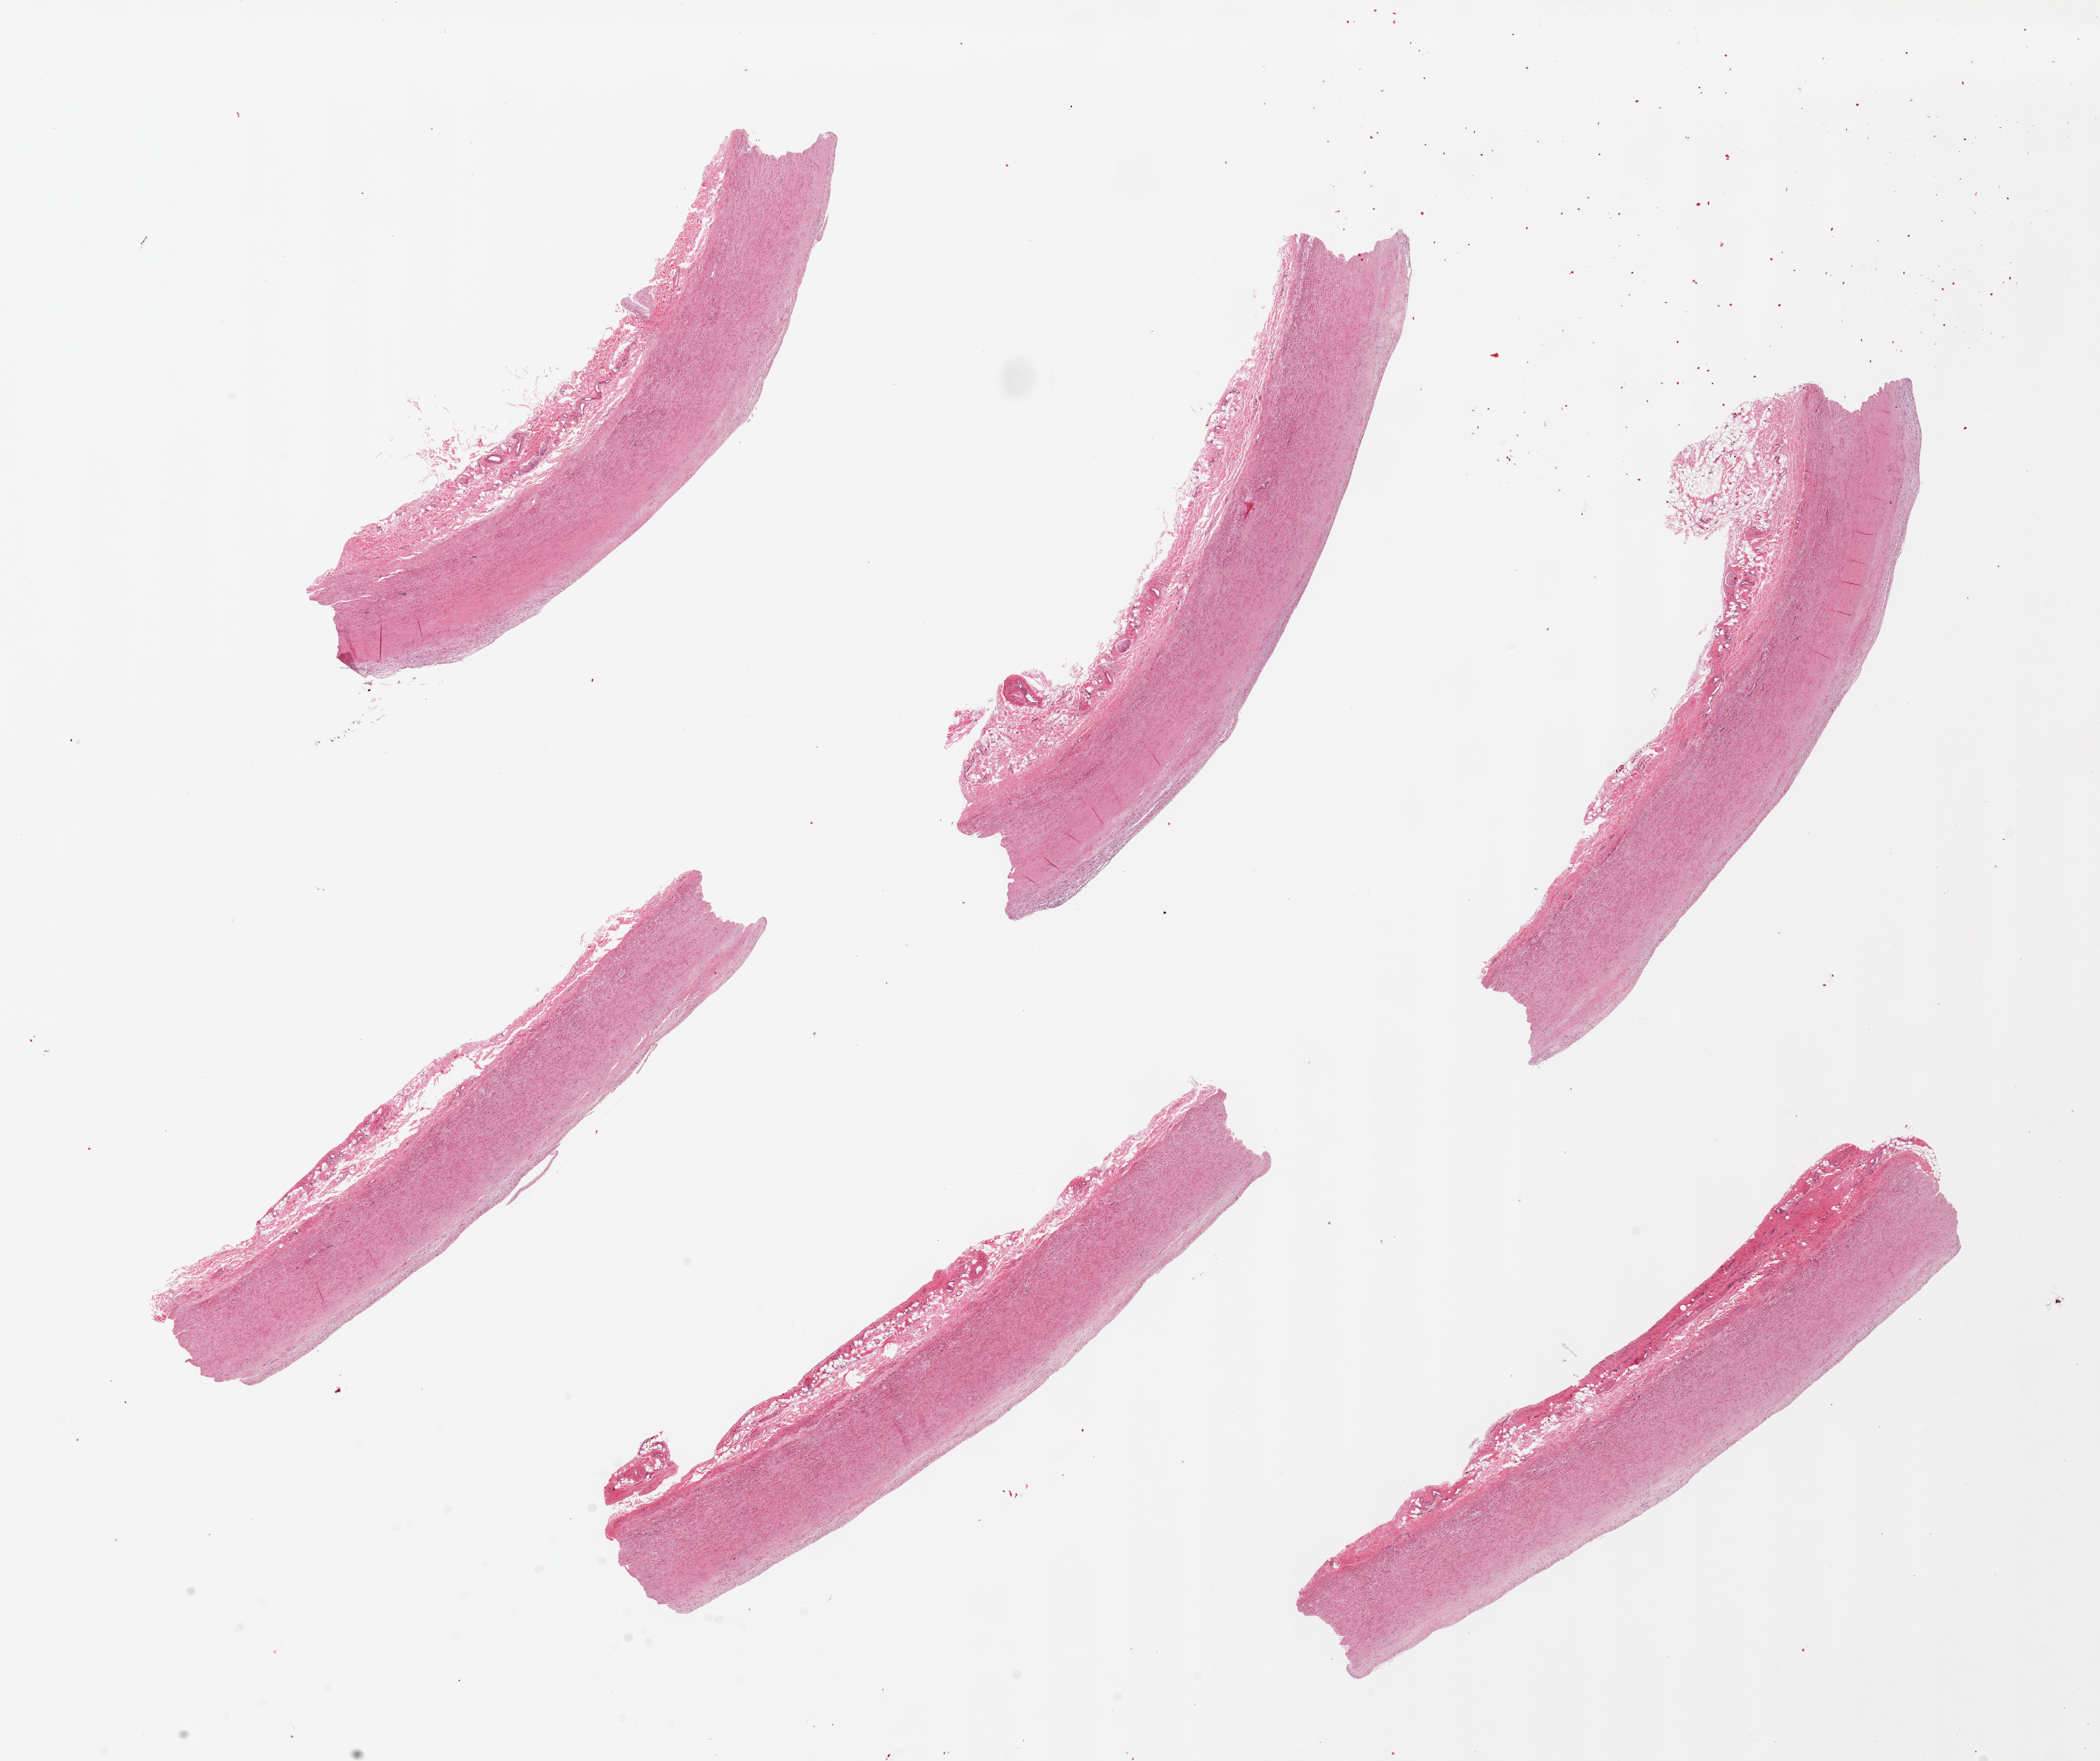
Whole-slide image, hematoxylin and eosin (H&E) stain, a low-resolution overview of the entire scanned area, about 25.6 x 21.5 mm, PAXgene-fixed, paraffin-embedded tissue, sampled site (target tissue): aorta, donor tissue sample. Male donor.
Review note (as recorded): 6 pieces. Thin intimal plaques.